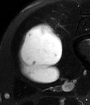
MRI of an extremity soft-tissue mass, one axial slice; position 22 of 65 along the scan axis; T2-weighted fat-saturated; MR volume resampled by the dataset authors to the PET/CT grid (not the native acquisition matrix); 3.27 mm slice thickness; 90 × 105 image matrix, field of view 88 × 103 mm. Male patient. From the clinical record (not read from this slice): histological type: mixoid liposarcoma; grade: low; site of the primary tumour: left thigh.
Structures marked on this image (expert contour drawn on MRI and transferred to this co-registered scan by the dataset authors):
- gross tumour volume (mass): bounding box <18,22,63,83> (left, top, right, bottom; pixels)